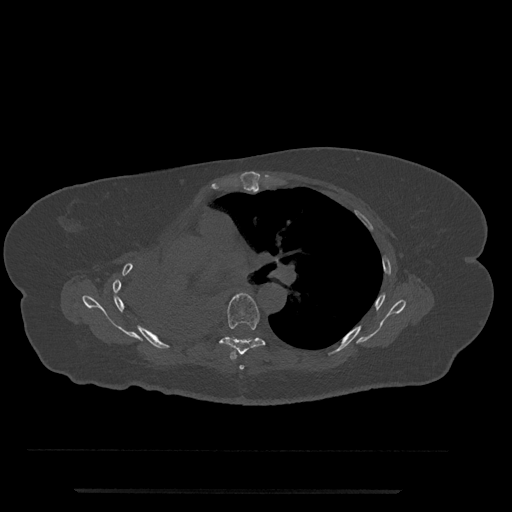
CT including the spine, one axial slice; position 495 of 797 along the scan axis; bone window (W 1800 / L 400 HU); 0.5 mm slice thickness; 512 × 512 image matrix, field of view 440 × 440 mm. Female patient, age 51 years. From the clinical record (not read from this slice): primary cancer: neuro.
Structures marked on this image (semi-automatically segmented with operator editing):
- T5 vertebra: bounding box (x1, y1, x2, y2) in pixels: (239, 365, 244, 370)
- T6 vertebra: (219, 293, 272, 360)